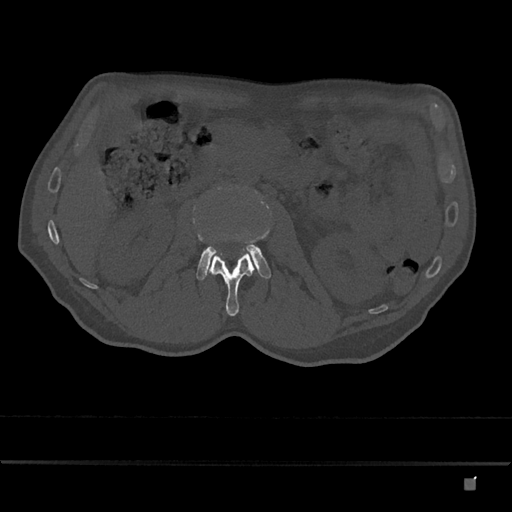
CT including the spine, one axial slice. Slice 448 of 797 in the series (ordered by position). Reconstruction kernel Br40s/3. Bone window (W 1800 / L 400 HU). 0.5 mm slice thickness. 512 × 512 image matrix, field of view 390 × 390 mm. Patient: male, 72 years. From the clinical record (not read from this slice): primary cancer: prostate.
Outlined on this slice (semi-automatic segmentation, software-assisted and operator-edited):
- L2 vertebra: bounding box (x1, y1, x2, y2) in pixels: (207, 250, 254, 316)
- L3 vertebra: (196, 244, 271, 280)